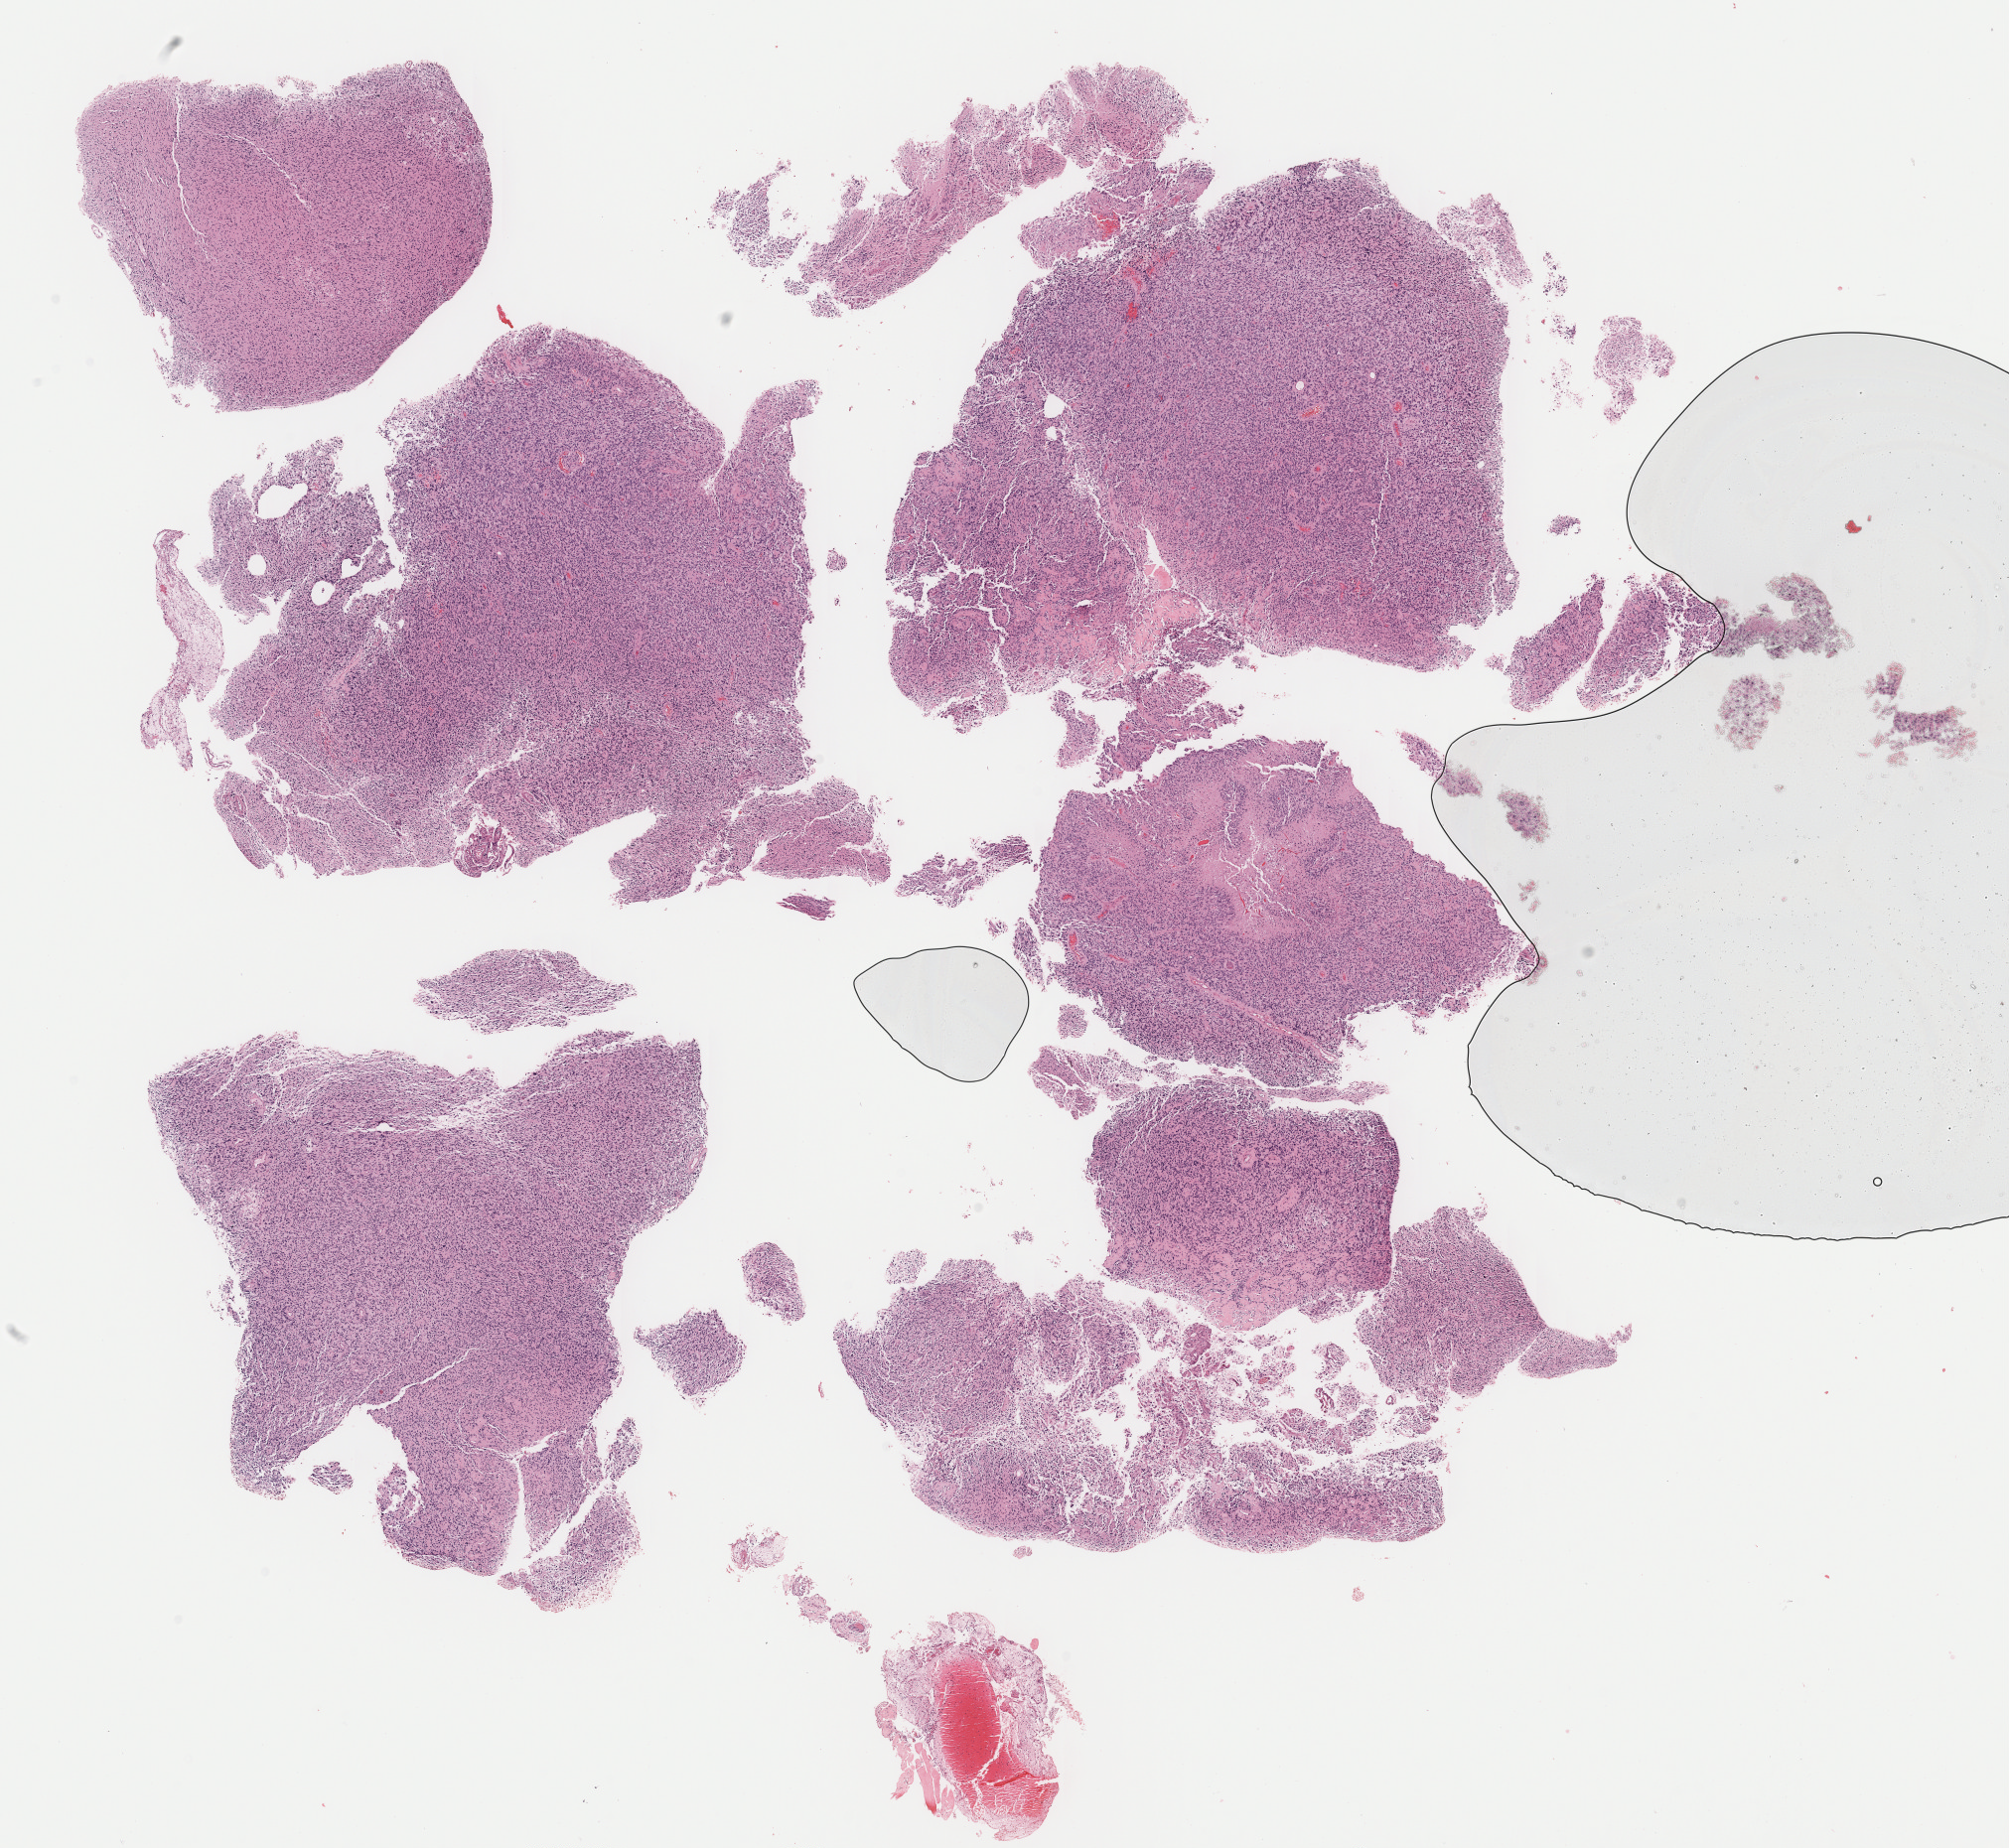
H&E-stained whole-slide image, a low-resolution overview of the entire scanned area, about 15.9 x 14.7 mm (from a 40x scan); FFPE section; sample: primary tumour, brain. Patient: female, age at initial diagnosis 36 years.
Histologic diagnosis: Glioblastoma.